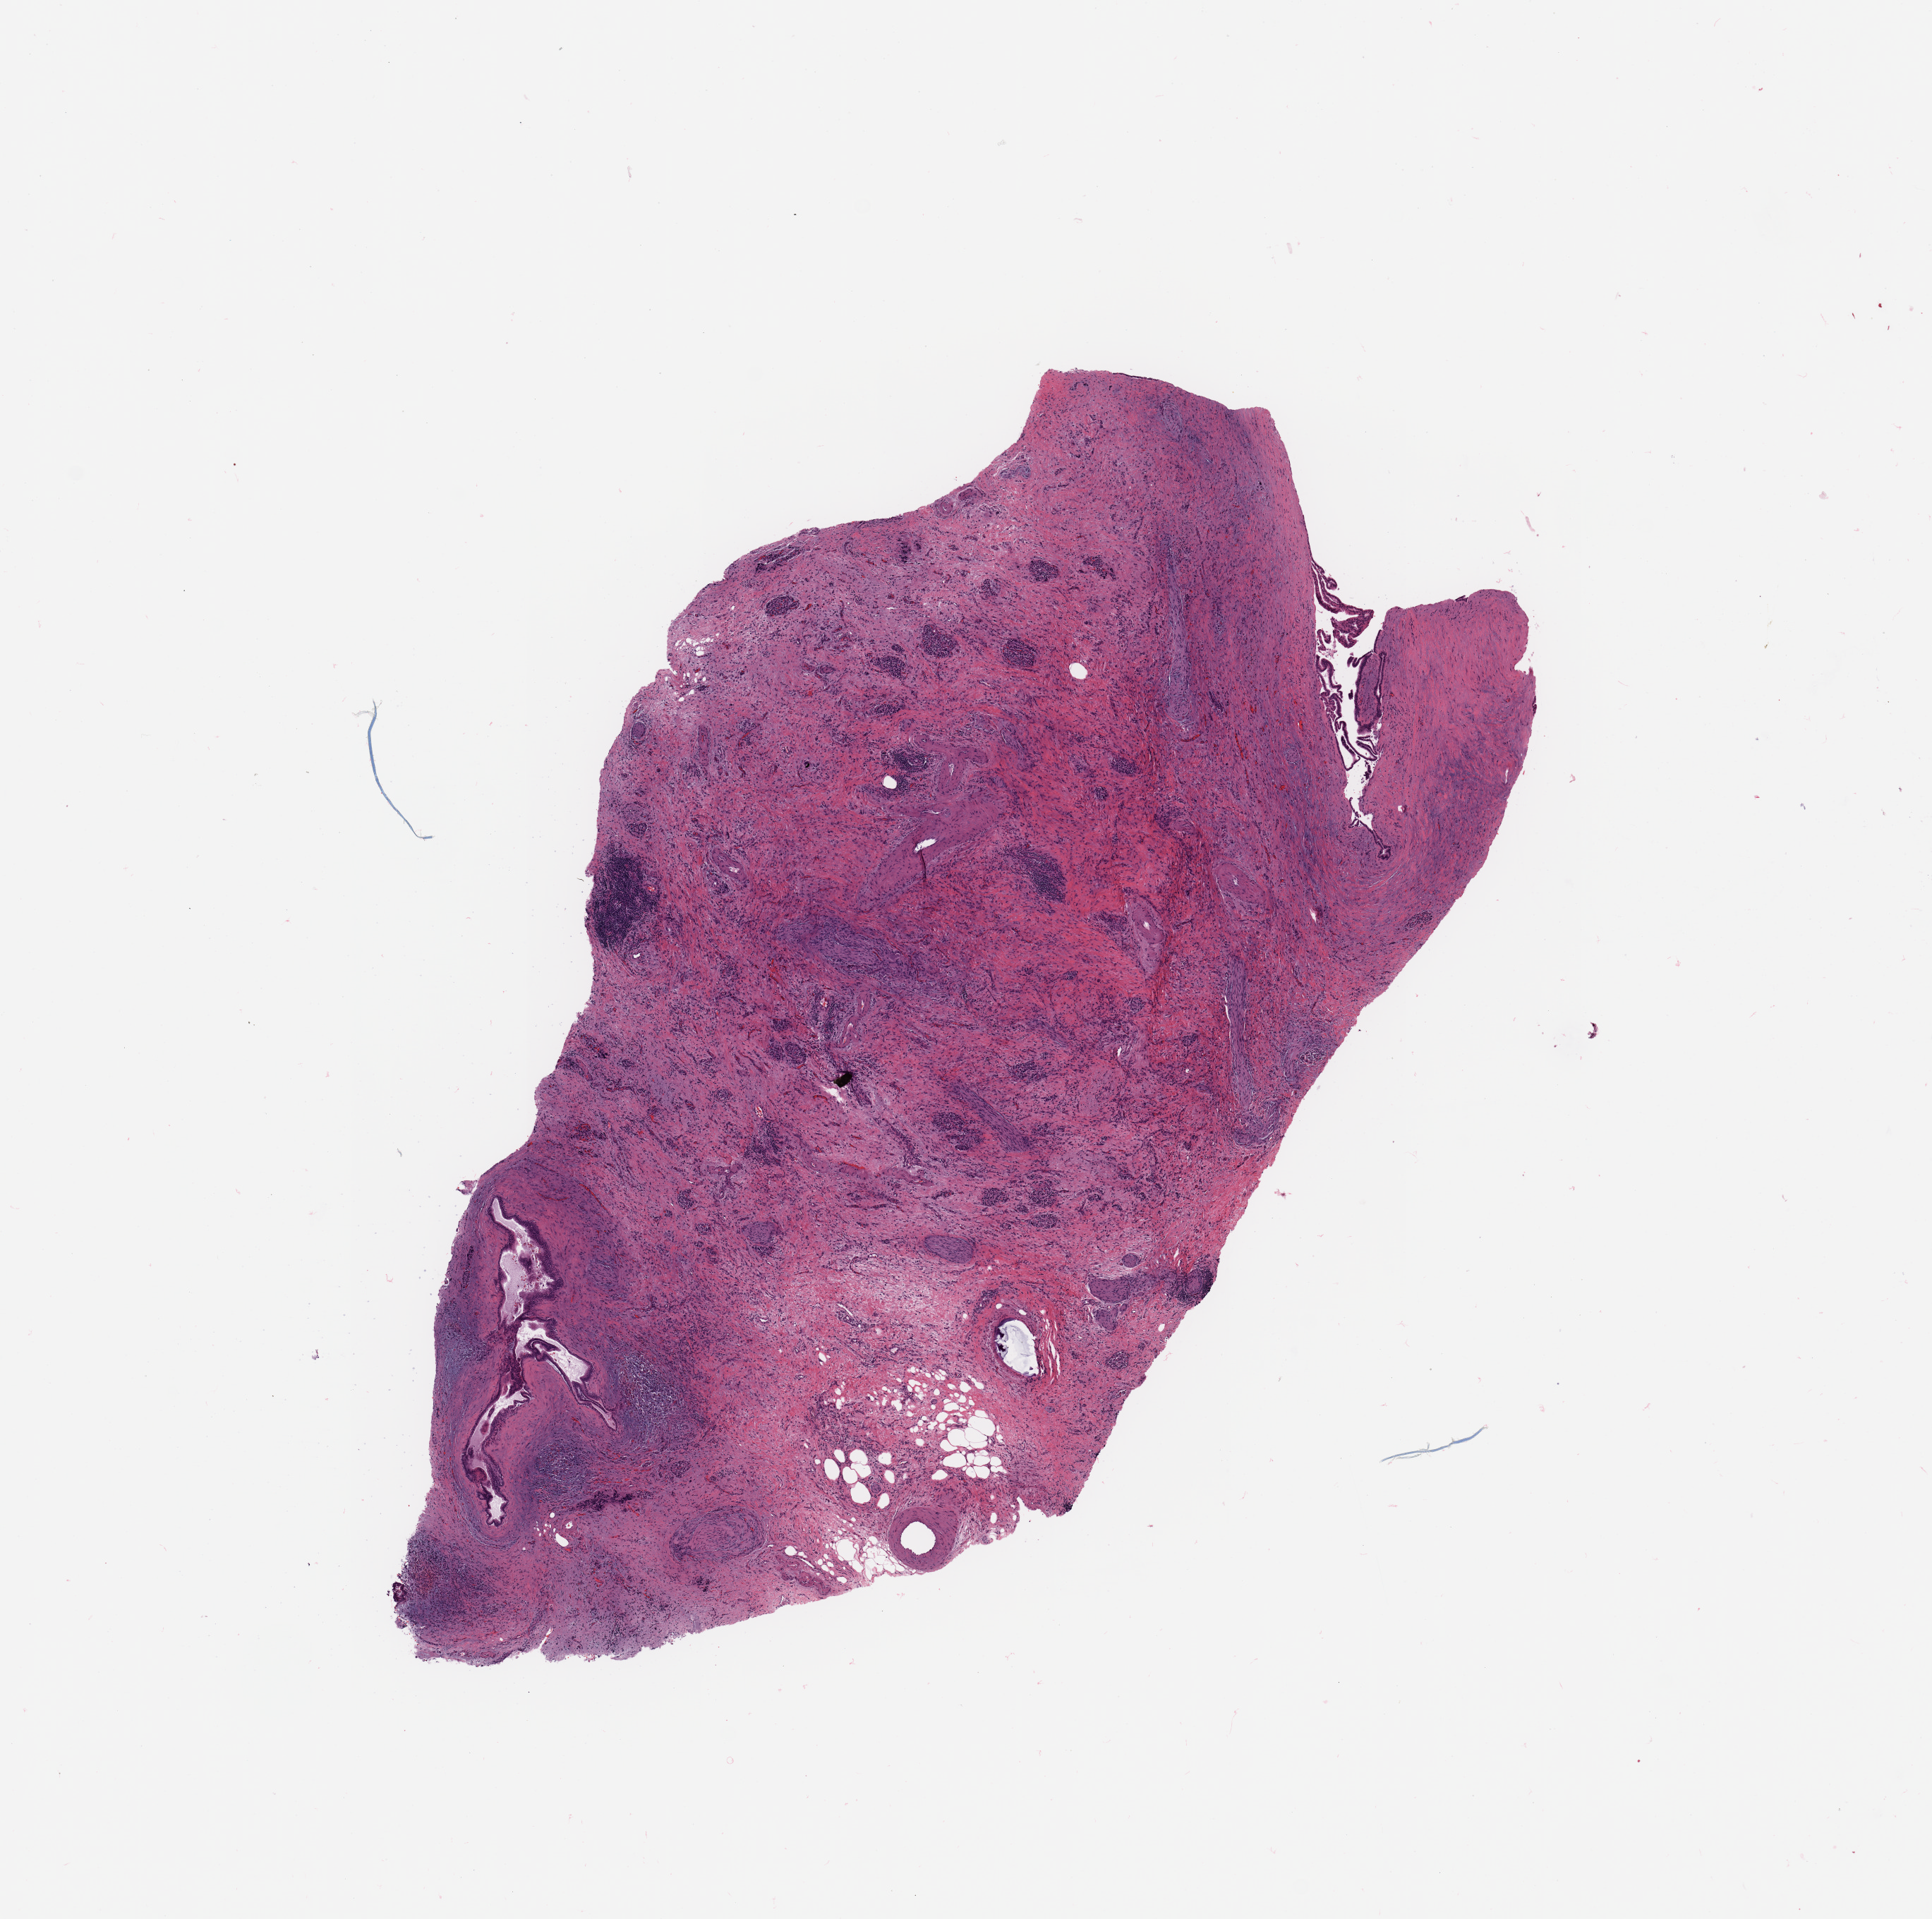
H&E-stained whole-slide image — low-resolution overview of the scanned area, about 10.8 x 10.8 mm (slide scanned at 20x); normal (non-tumour) tissue sample, sampled site: pancreas. Male, 84 y/o.
This section: normal (non-tumour) tissue from the same patient. Patient diagnosis: Infiltrating duct carcinoma, NOS.